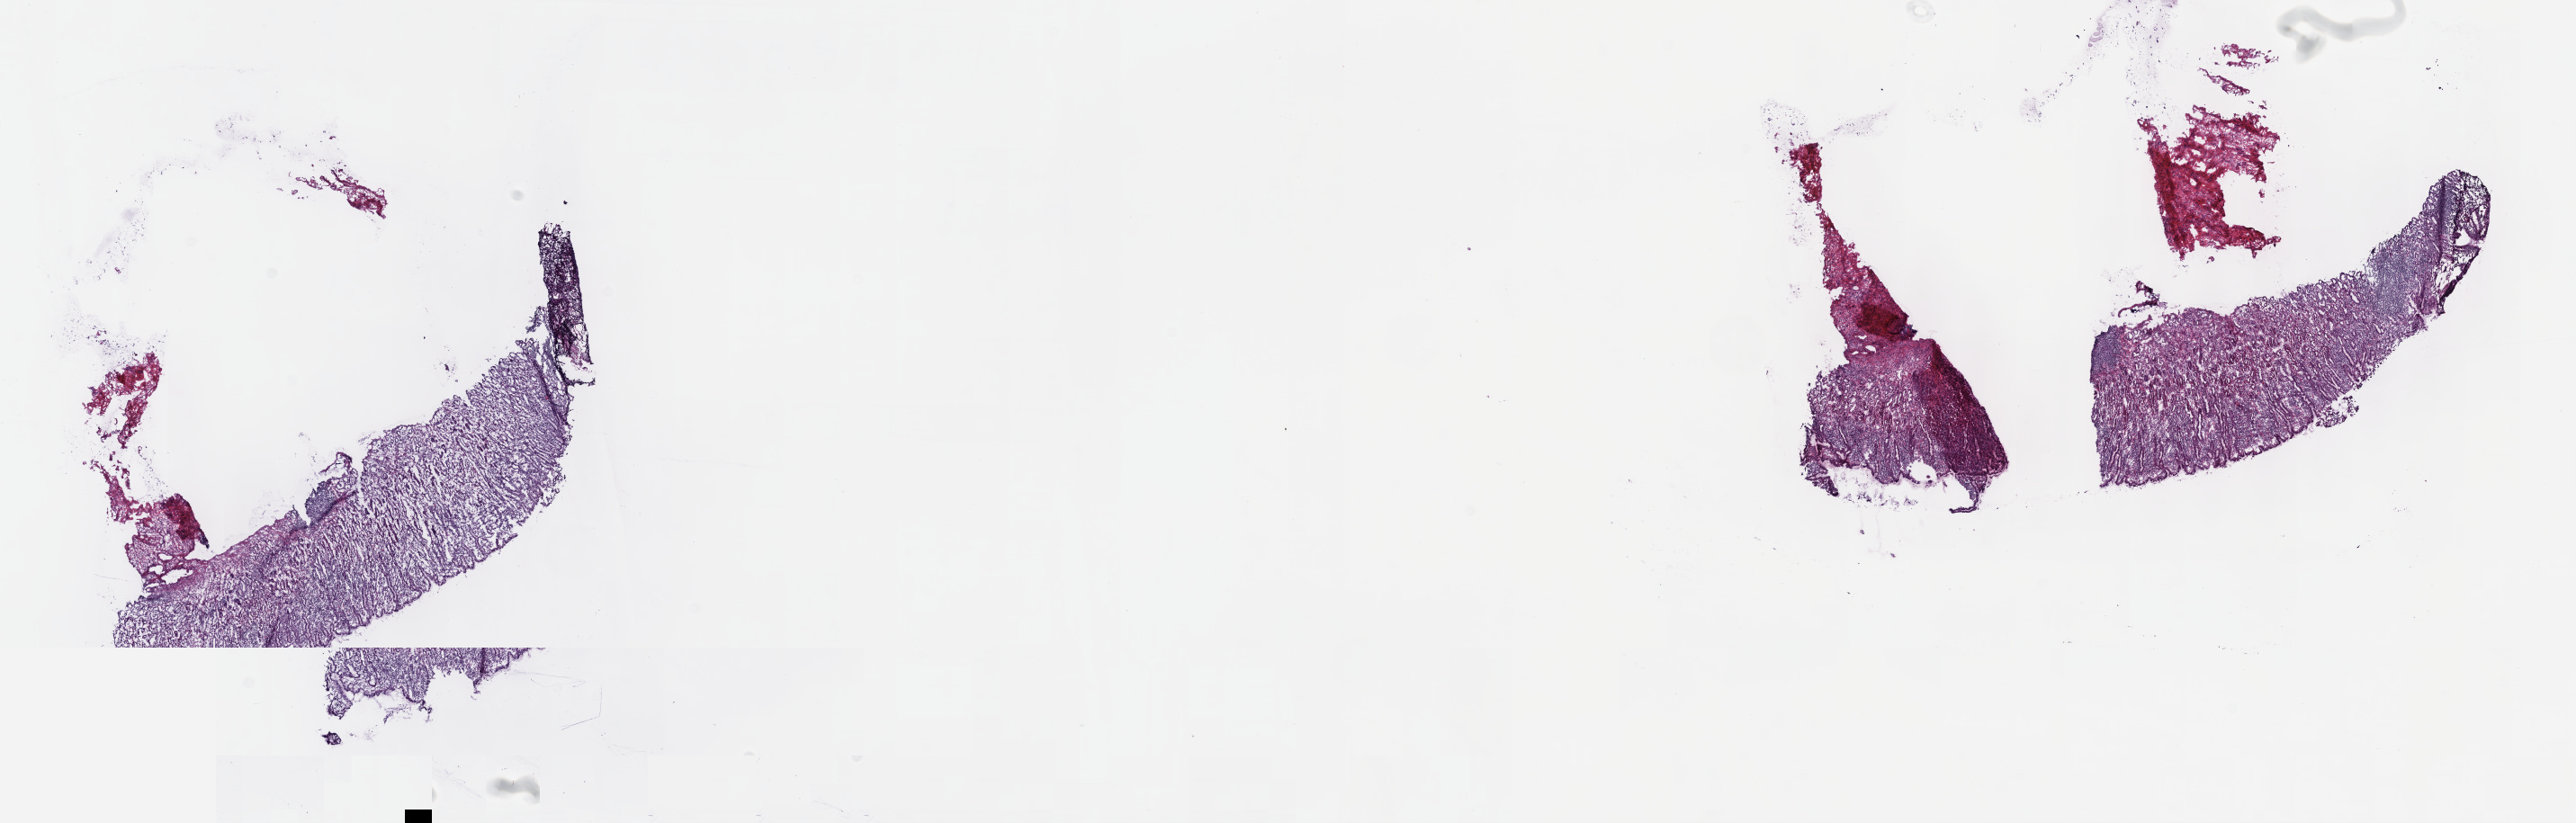
Whole-slide histology image, H&E, shown as a low-resolution overview of the whole scanned area (about 23.2 x 7.4 mm, slide scanned at 40x). Frozen section from the top of the tissue portion. Primary tumour sample from the stomach. Female patient; age at initial diagnosis 53 years. Histologic grade: G3 (poorly differentiated). Composition of this section per pathologist review: tumour cells 100%, tumour nuclei 60%, normal cells 0%, stromal cells 0%, necrosis 0%. Inflammatory infiltration, as recorded: lymphocyte infiltration 8%, monocyte infiltration 0%, neutrophil infiltration 0%.
Histologic diagnosis: Carcinoma, diffuse type (fundus of stomach). AJCC pathologic stage: IIIB (6th edition). Lymph nodes positive (case pathology): 10 of 36 examined.